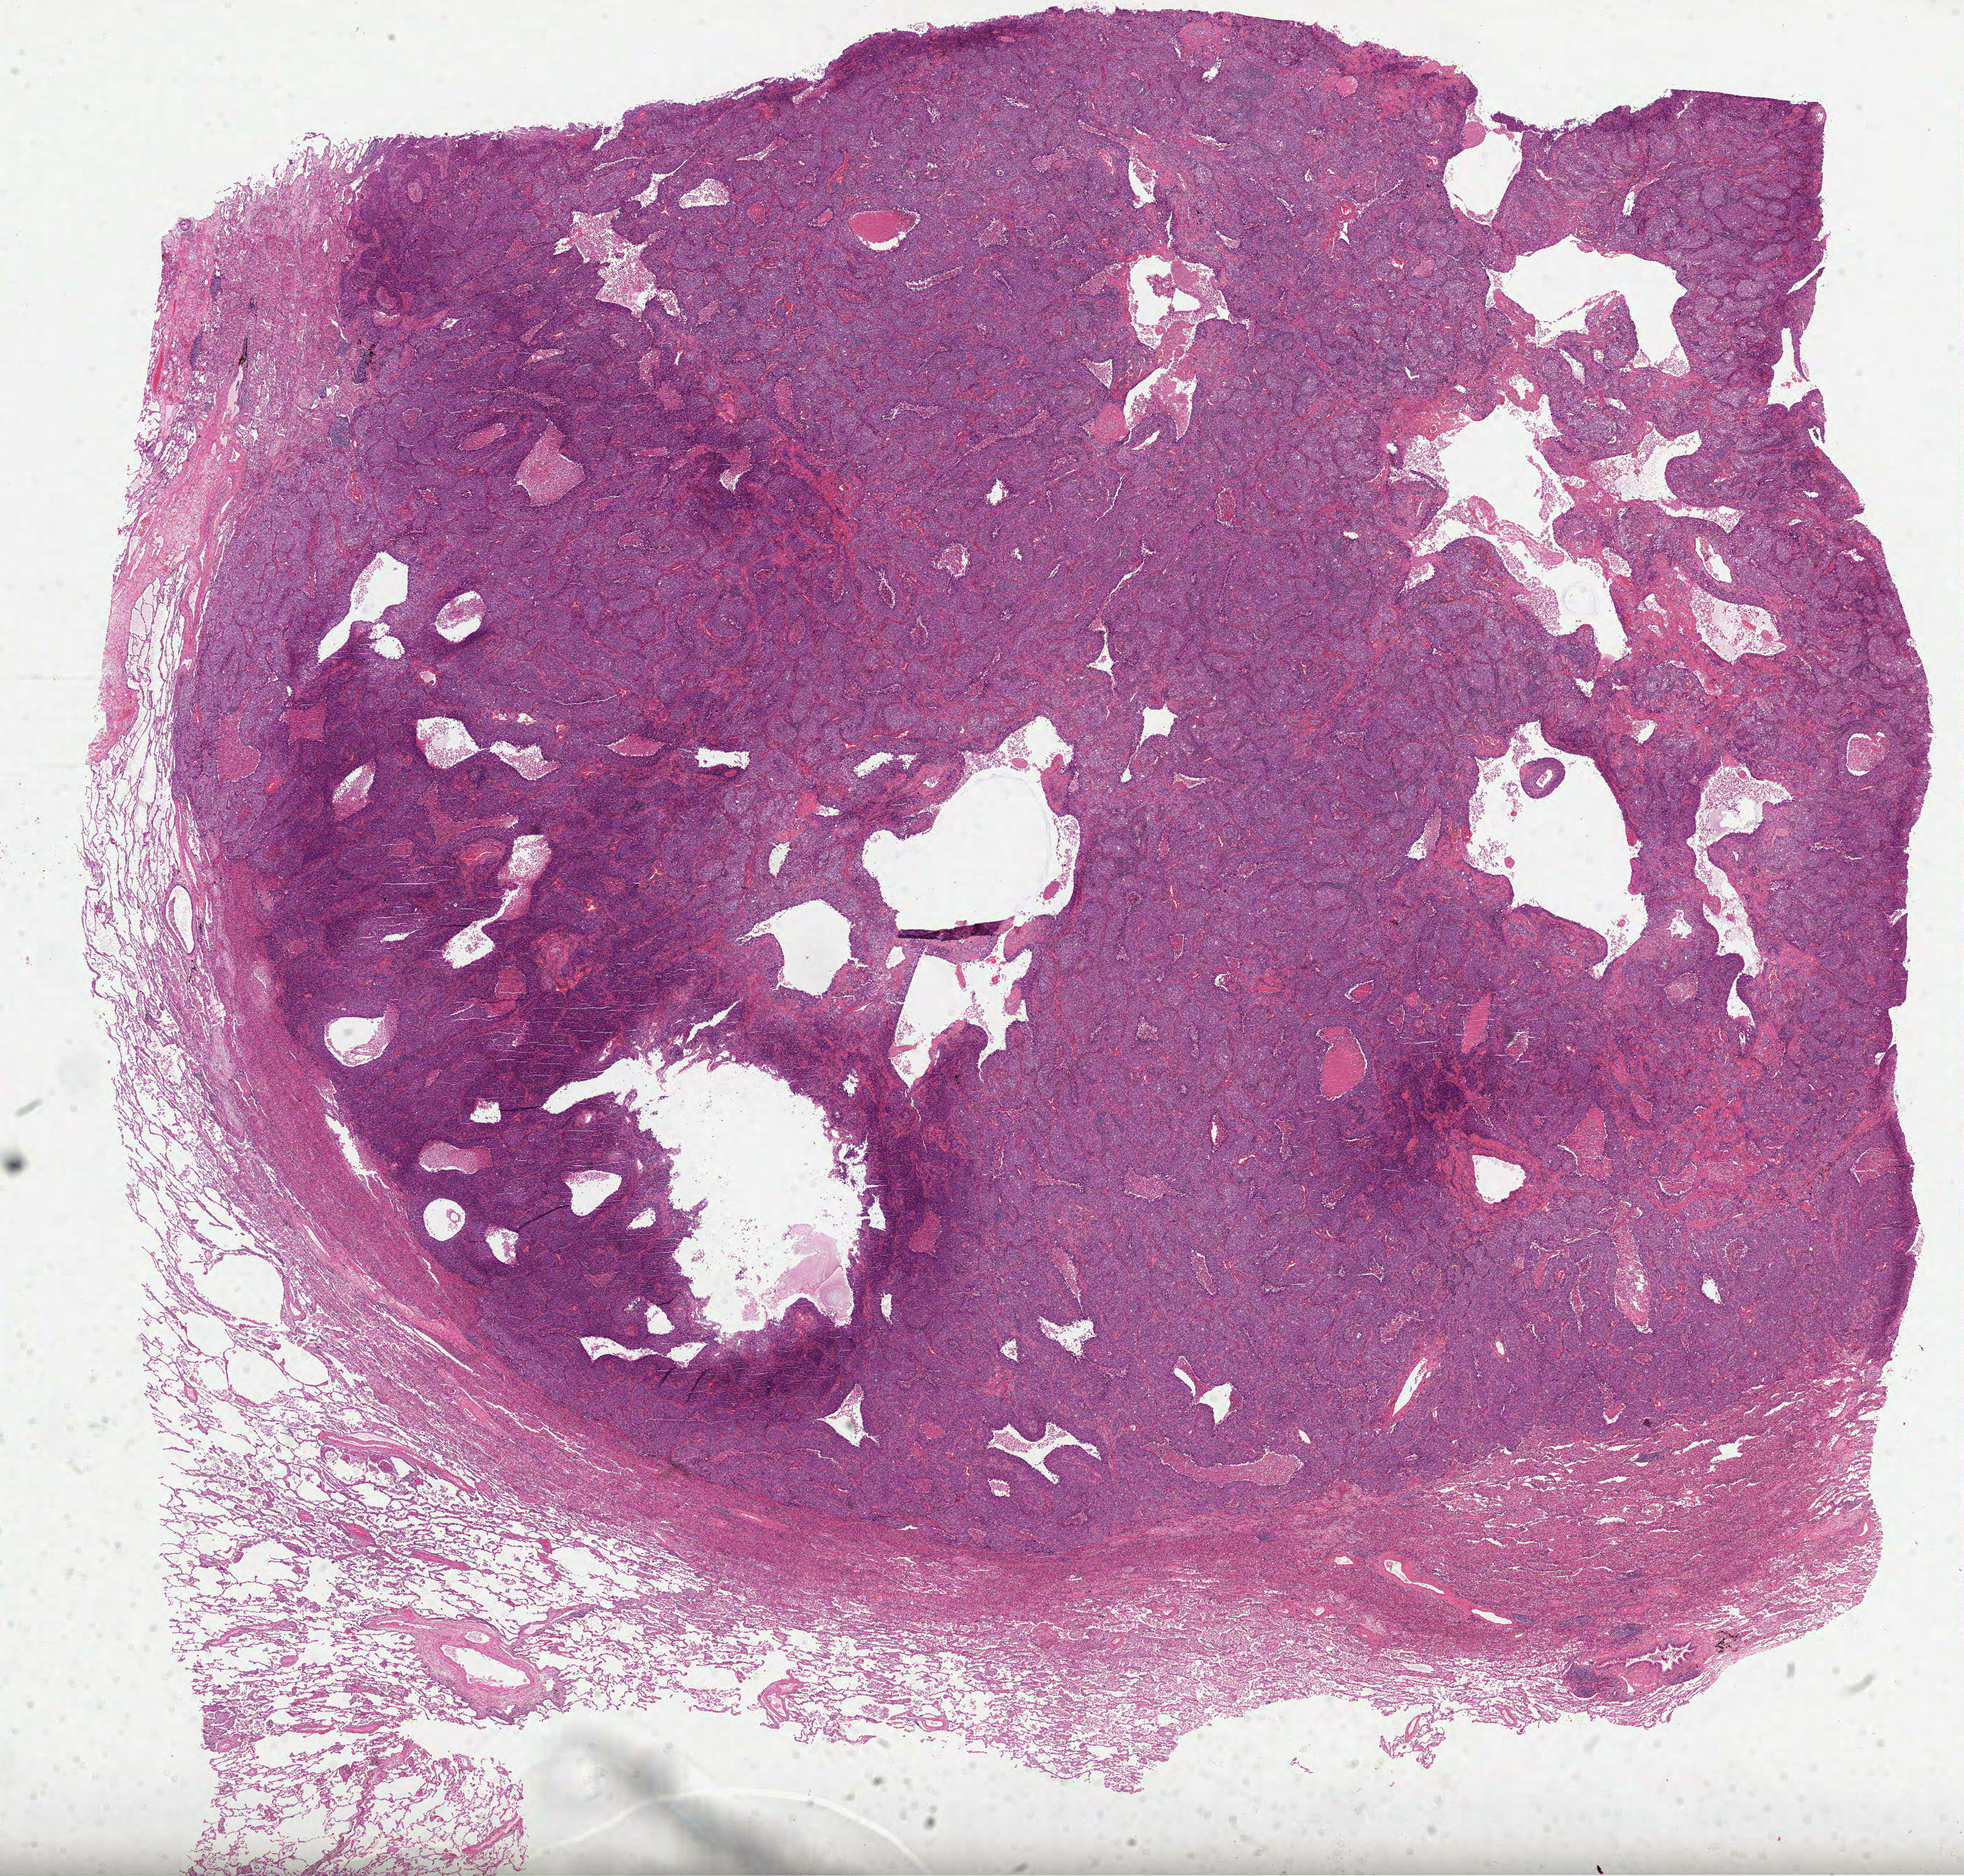
Digitized H&E tissue section (whole slide) — low-resolution overview of the scanned area, about 22.2 x 21.2 mm. FFPE section. Sample: primary tumour, lung. Patient: male, age at initial diagnosis 79 years.
AJCC pathologic stage: IIB. Diagnosis: Squamous cell carcinoma, NOS.